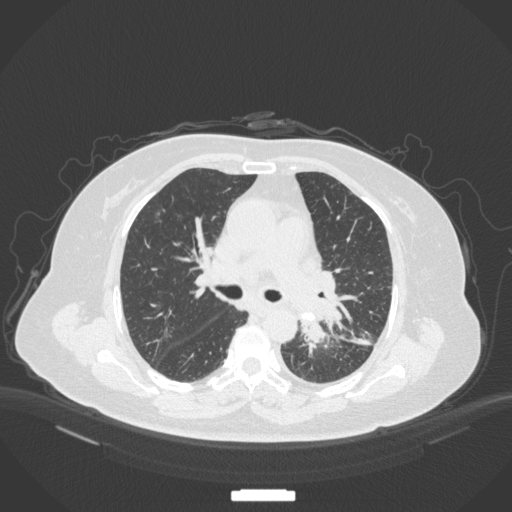
Chest CT, one axial slice. Slice 215 of 328 in the series (ordered by position). Reconstruction kernel B31f. 120 kVp. Lung window (W 1500 / L -600 HU). 1 mm slice thickness. 512 × 512 image matrix, field of view 400 × 400 mm. Patient: female, 69 years. From the clinical record (not read from this slice): clinical TNM (as recorded): T2b N3 M1.
Annotated regions visible in this slice (rectangle marked by the reading radiologist):
- lung tumour (recorded histology: adenocarcinoma): box from (x=298, y=310) to (x=327, y=353) px